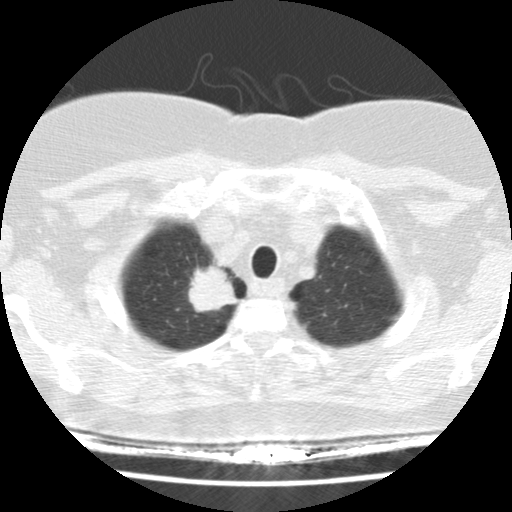
Low-dose screening chest CT, axial slice; baseline screening round; lung window (W 1500 / L -600 HU); 2.5 mm slice thickness; slice 17 of 148 in the series. Female participant, aged 58 years at enrolment. Former smoker at enrolment.
Lesion marked by an expert reader, bounding box <168,251,246,328> (left, top, right, bottom; pixels). Screening reader's record for this exam (one nodule recorded; not confirmed to be the boxed lesion): non-calcified nodule or mass ≥4 mm, right upper lobe, 28 × 24 mm, spiculated (stellate) margins, soft tissue attenuation.